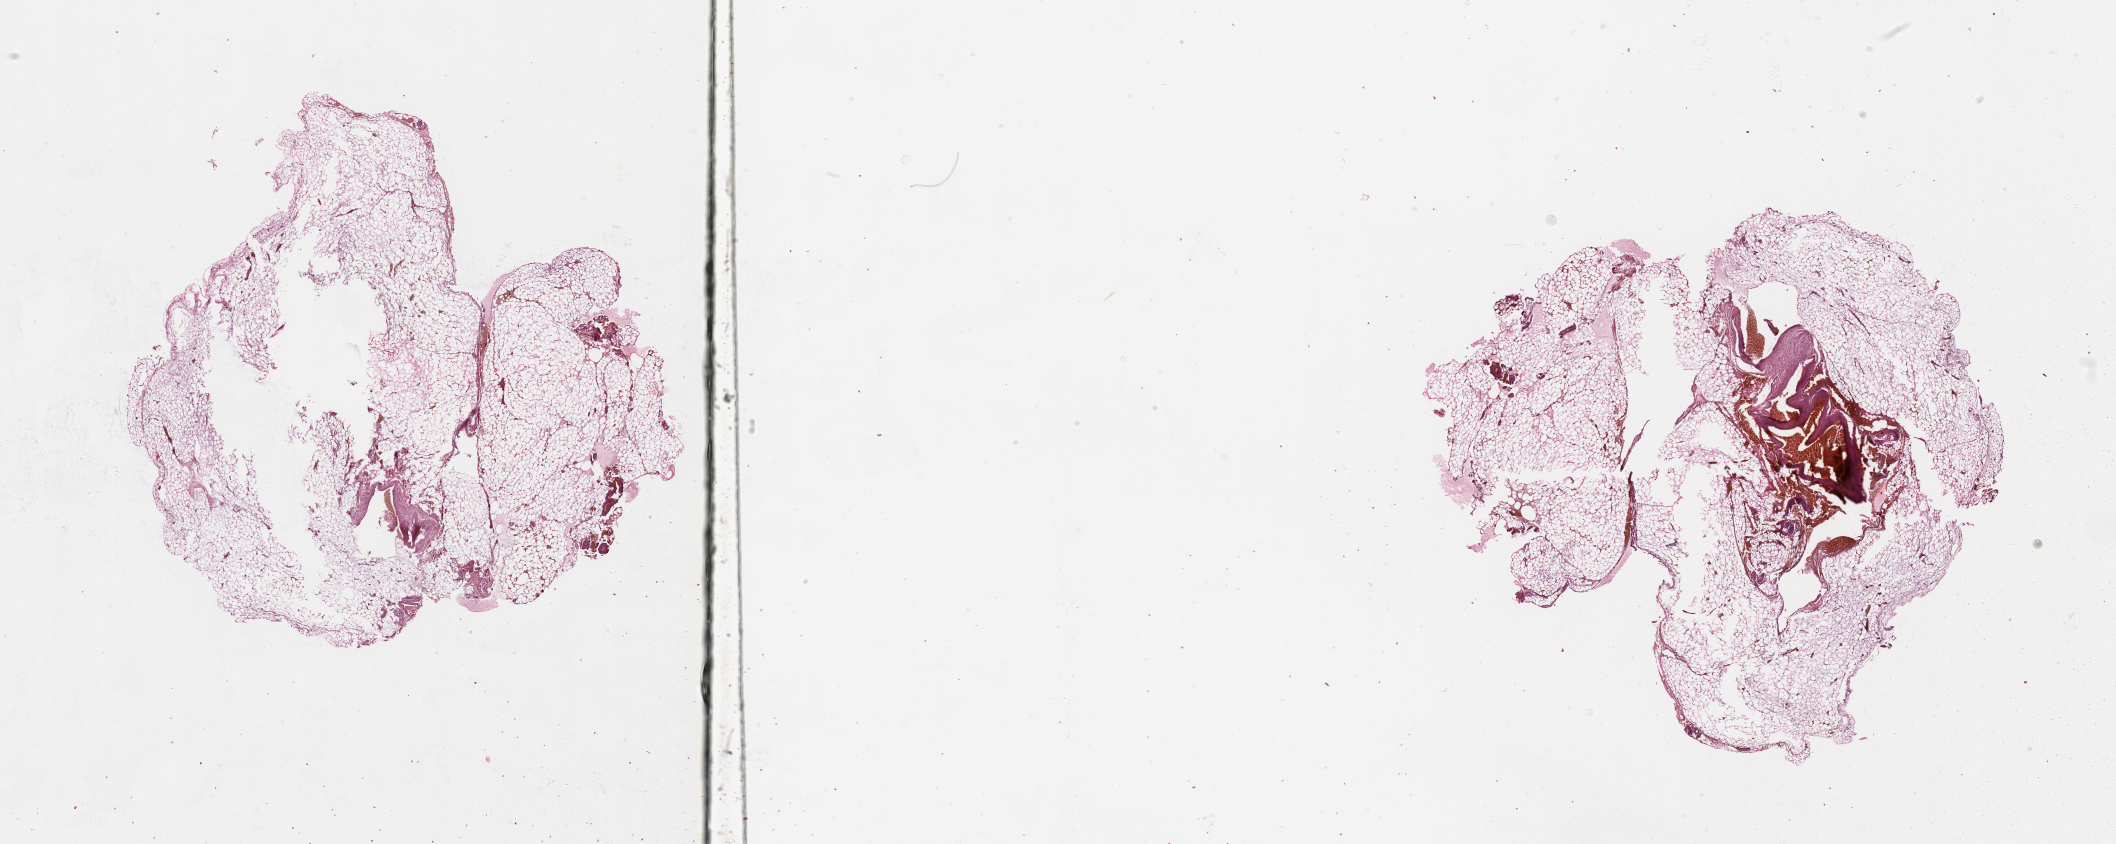
H&E whole-slide image, whole scanned area (about 33.5 x 13.4 mm, acquisition: 20x scan) shown as a low-resolution overview. Normal (non-tumour) tissue sample, sampled site: lymph node. 62-year-old male patient.
* this section: normal (non-tumour) tissue from the same patient
* patient diagnosis: Malignant melanoma, NOS